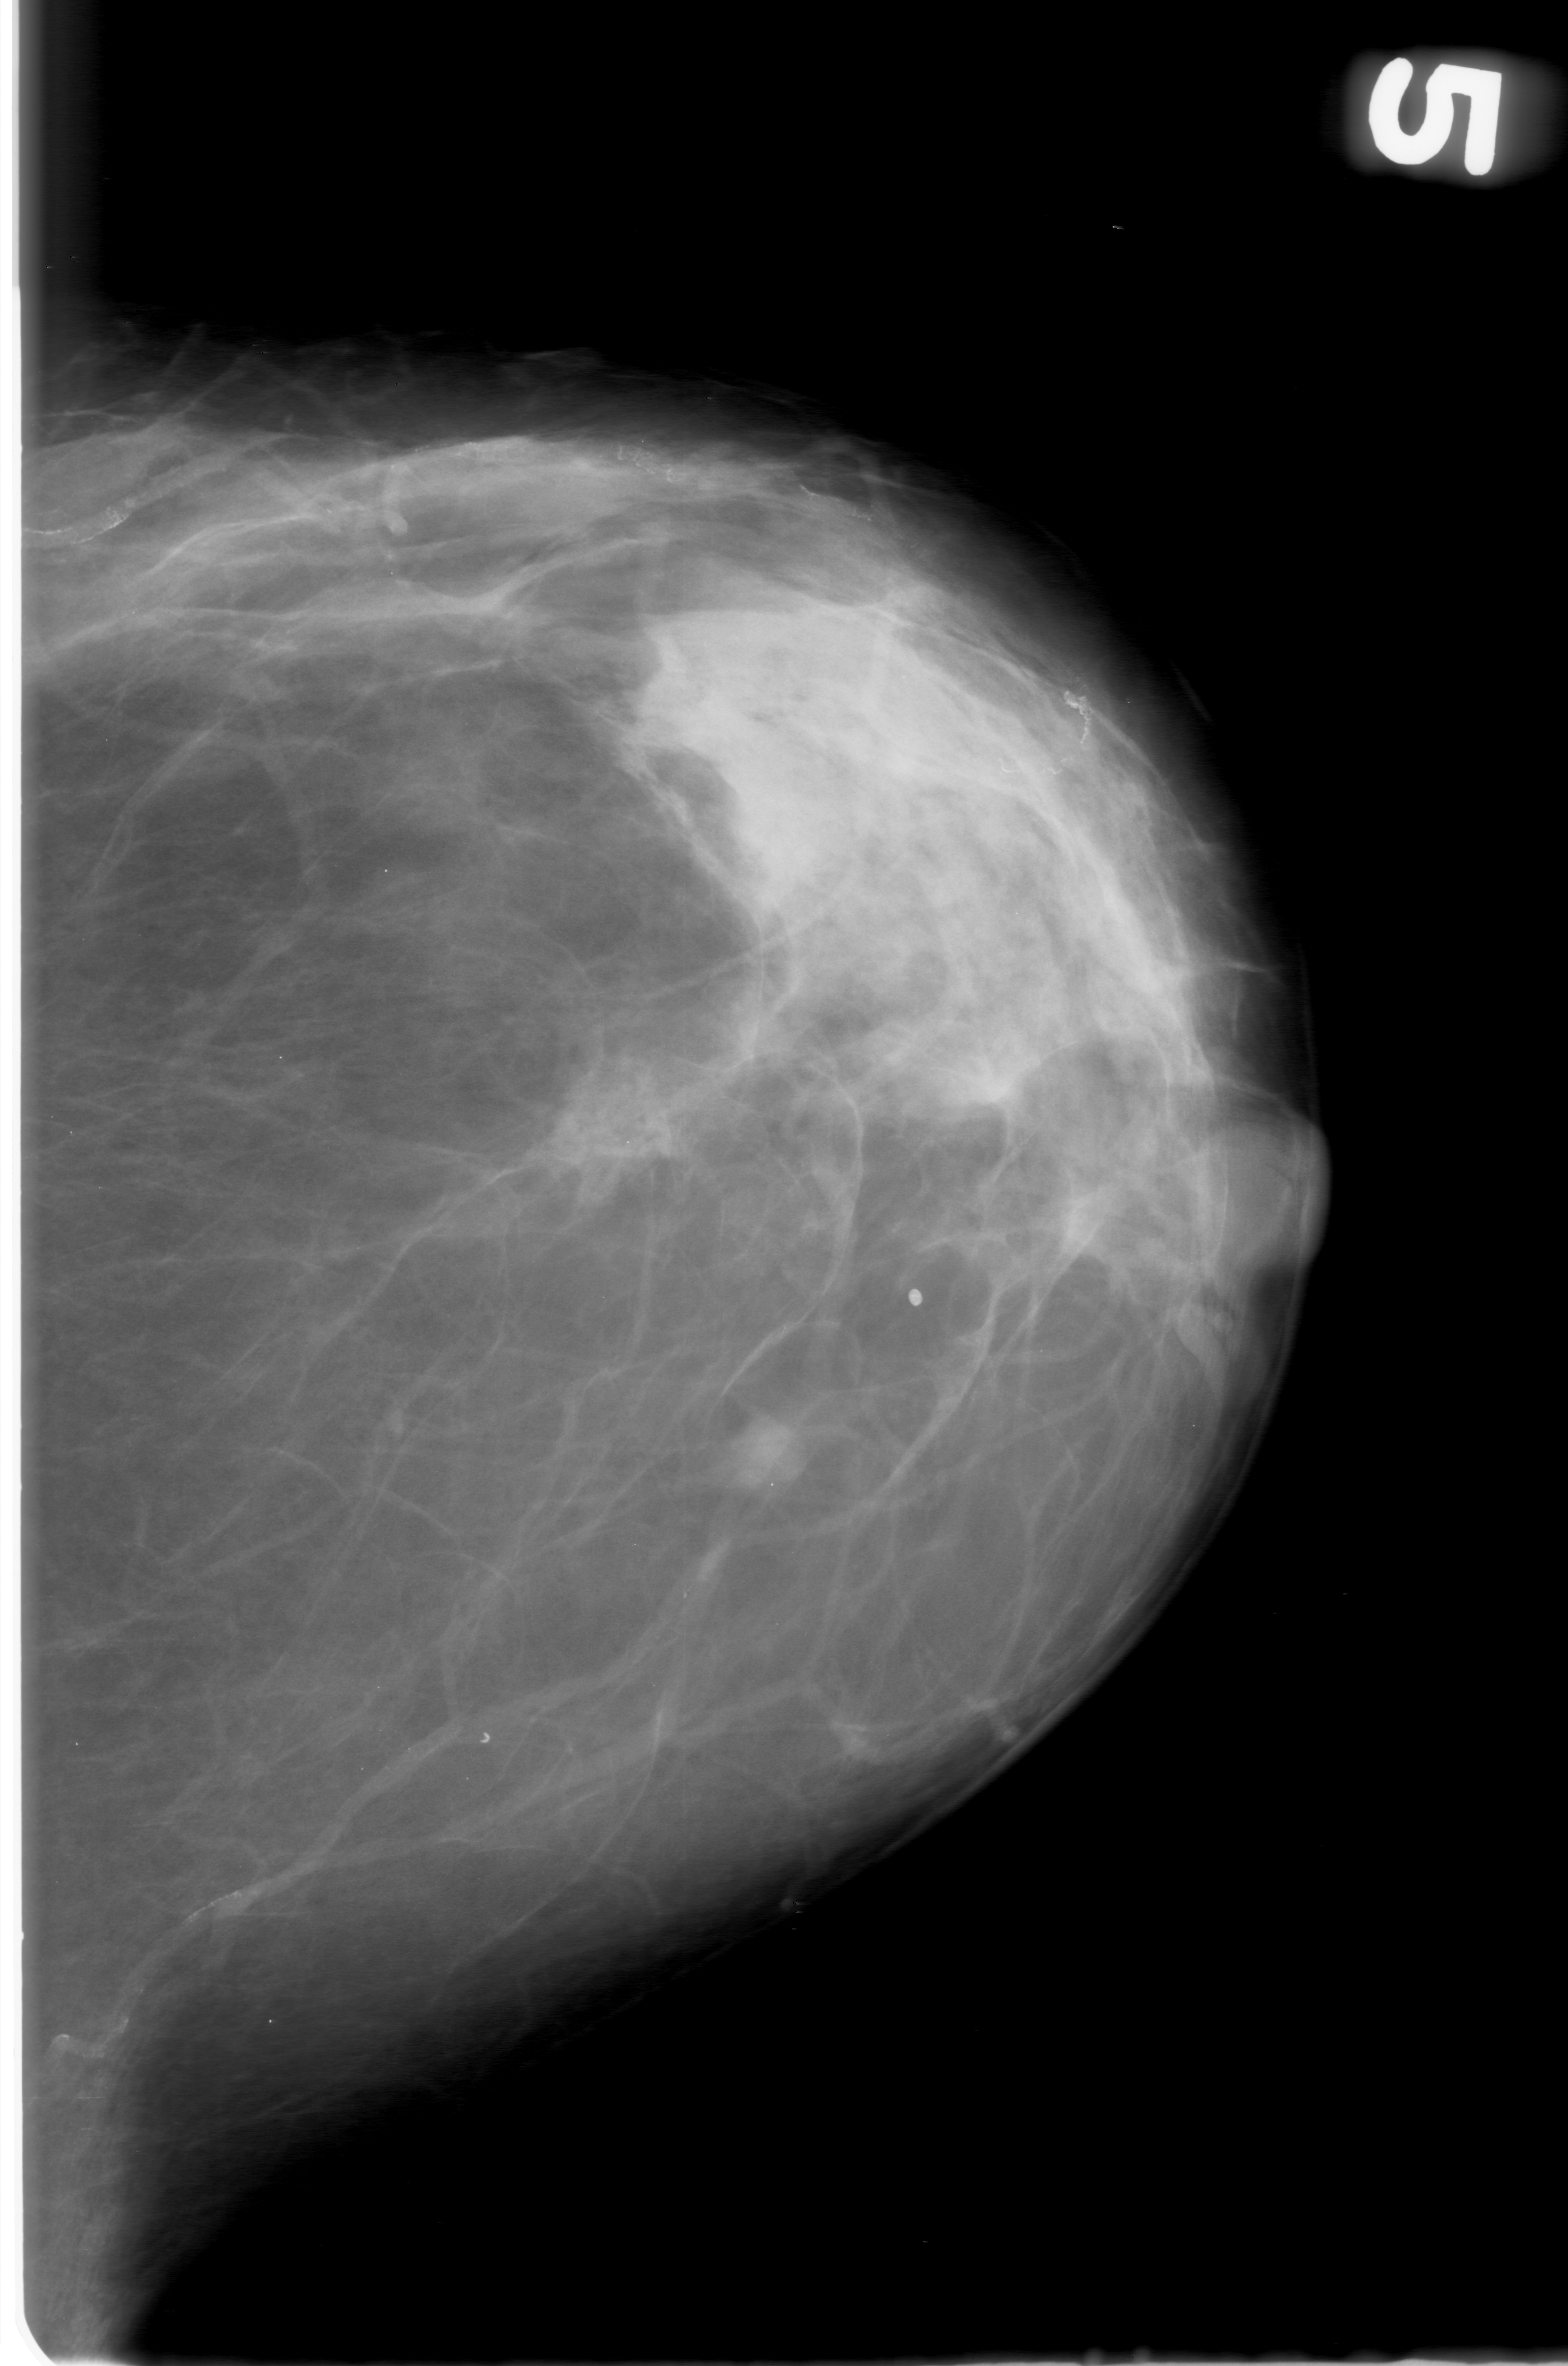
Scanned film-screen mammogram, left breast, CC view, BI-RADS breast density category 2 (scale 1–4).
Abnormality record for this image: mass, shape round, margins obscured; BI-RADS assessment category 0 (incomplete: needs additional imaging); pathology (as recorded): benign.